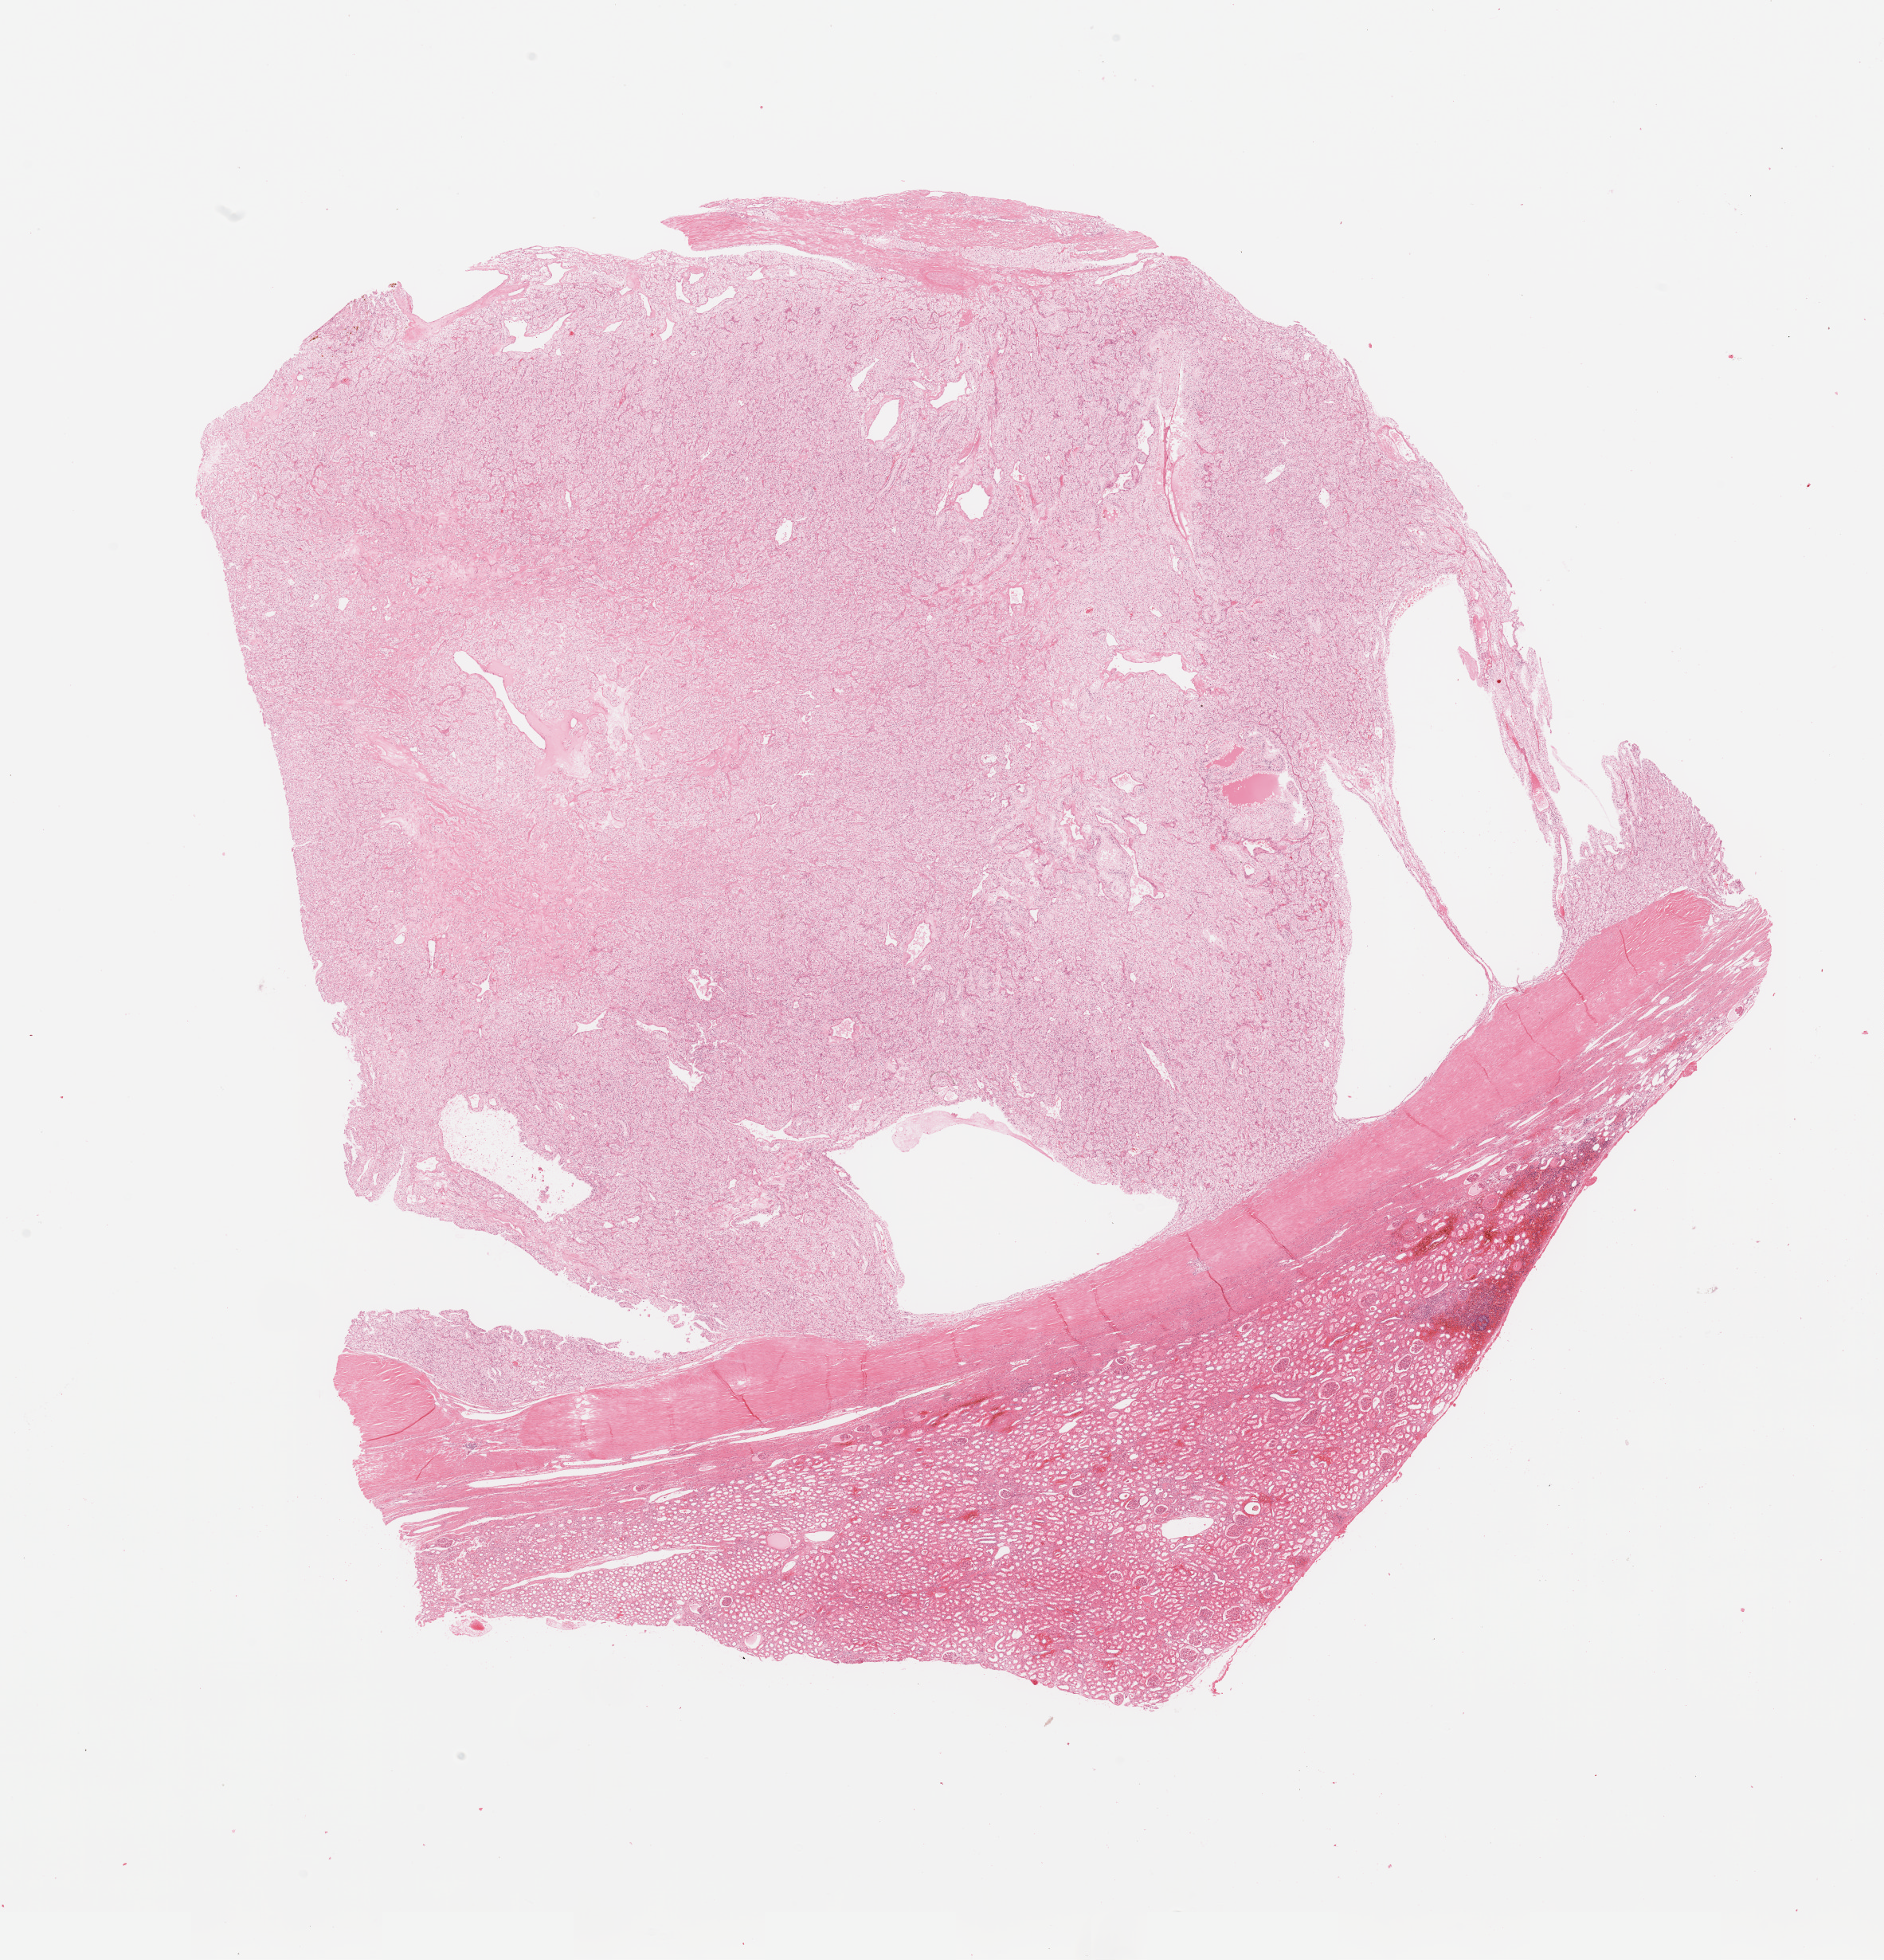
H&E-stained whole-slide image, a low-resolution overview of the entire scanned area, about 18.7 x 19.5 mm (slide scanned at 20x), kidney, tumour tissue. 51-year-old male patient. Histologic grade: G2 (moderately differentiated).
Diagnosis: Renal cell carcinoma, NOS.